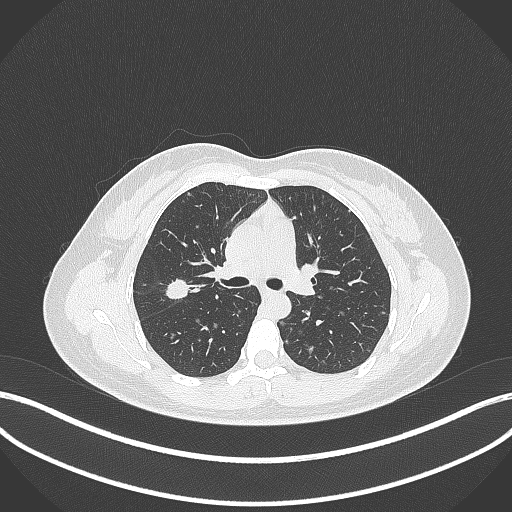
Chest CT, one axial slice; slice 211 of 307 in the series (ordered by position); lung window (W 1500 / L -600 HU); 1 mm slice thickness; 512 × 512 image matrix, field of view 400 × 400 mm. Female patient, age 33 years. Case-level facts recorded for this patient, not image findings: clinical TNM (as recorded): T1c N0 M0; histopathological grade: G2-G3.
Structures marked on this image (rectangle marked by the reading radiologist):
- lung tumour (recorded histology: adenocarcinoma): bounding box [x1, y1, x2, y2] px = [163, 274, 193, 301]